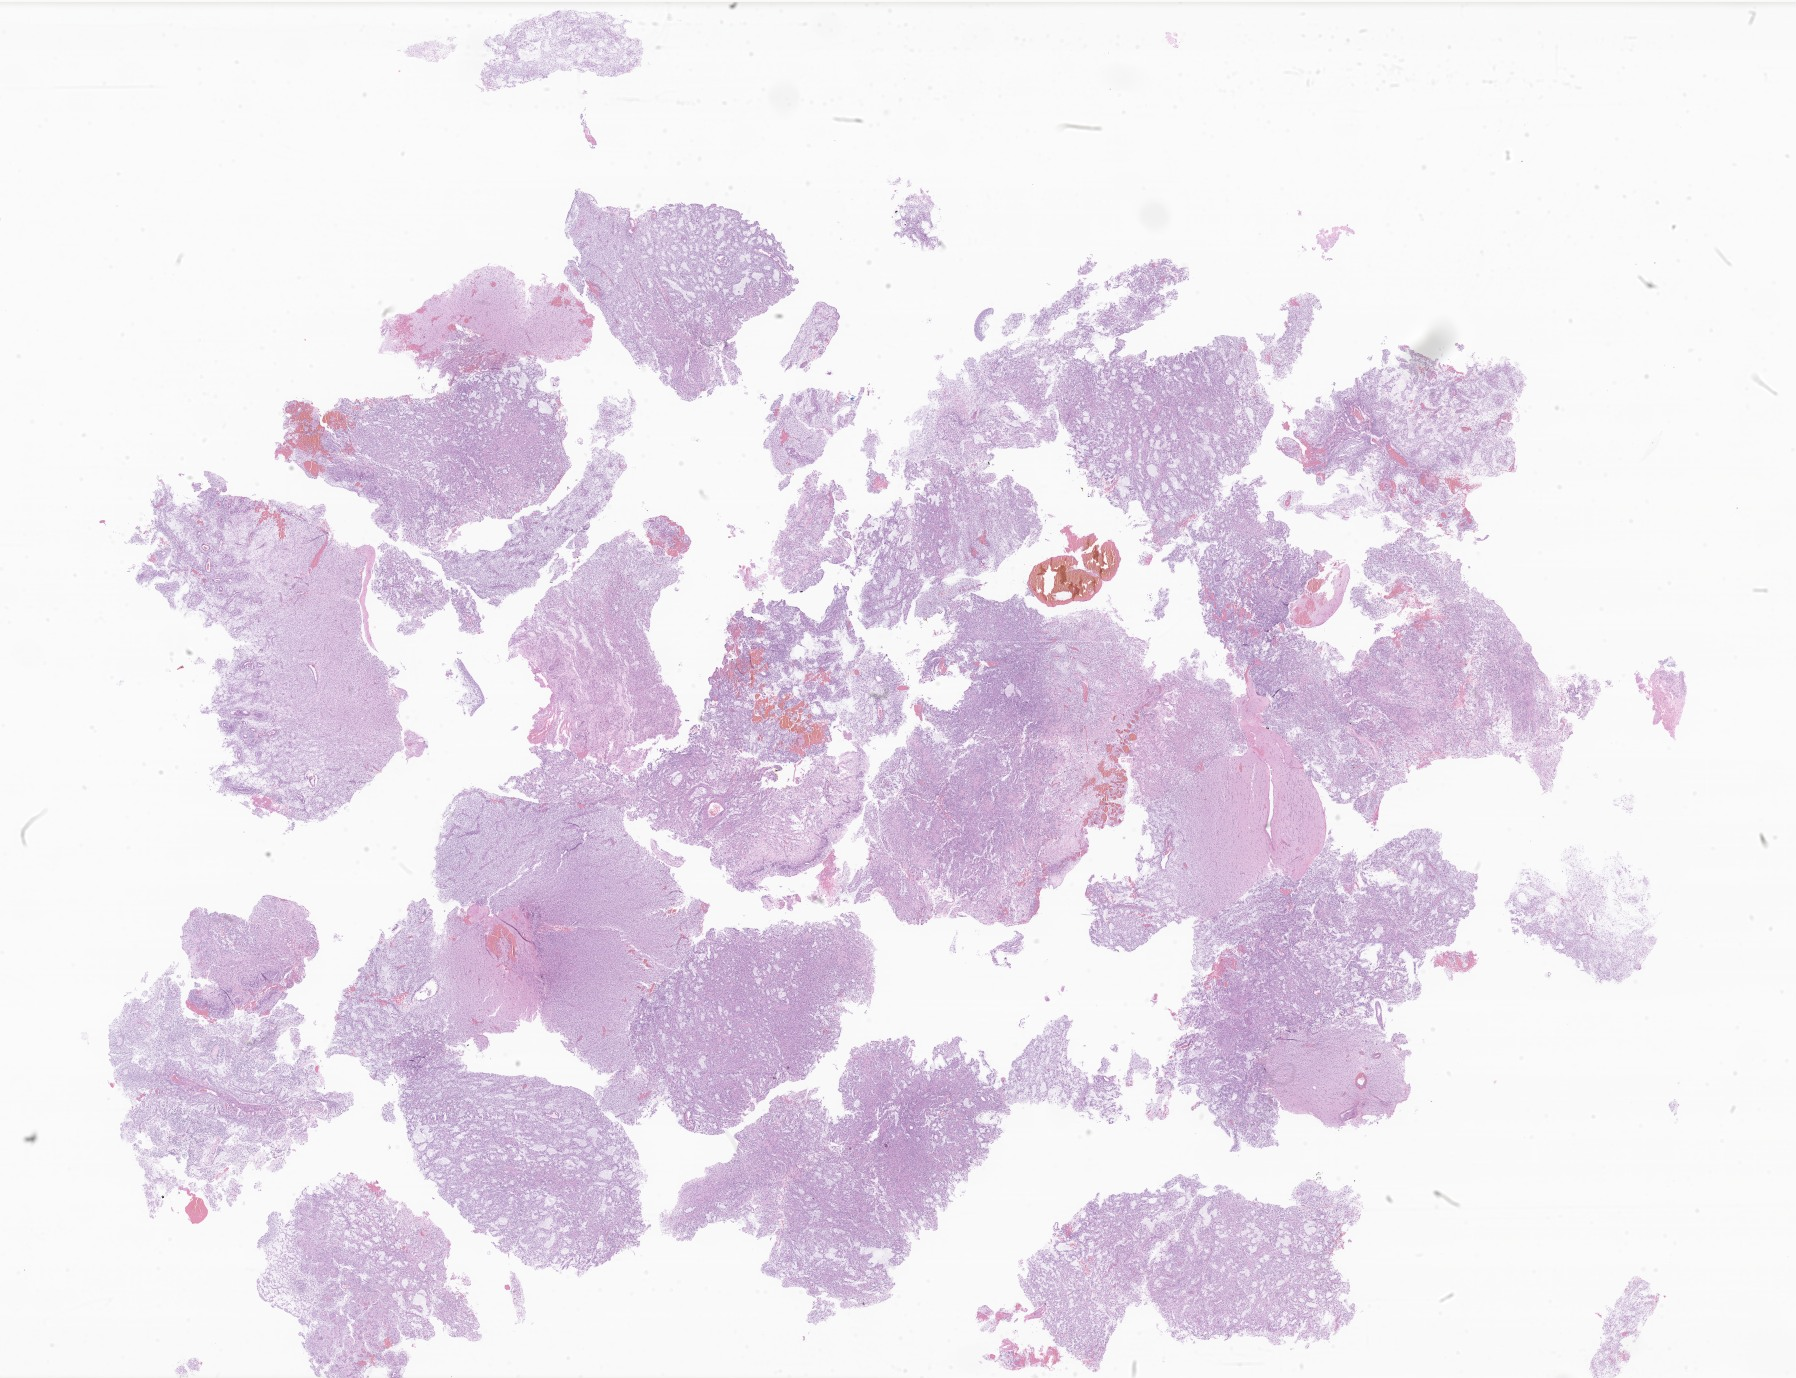
Digitized haematoxylin and eosin-stained section of tumor tissue from the brain — whole scanned area (about 30.3 x 23.2 mm) shown as a low-resolution overview. FFPE section. Patient male; age 112 months (9 years 4 months).
Diagnosis (ICD-O-3 morphology term): Astrocytoma, NOS.